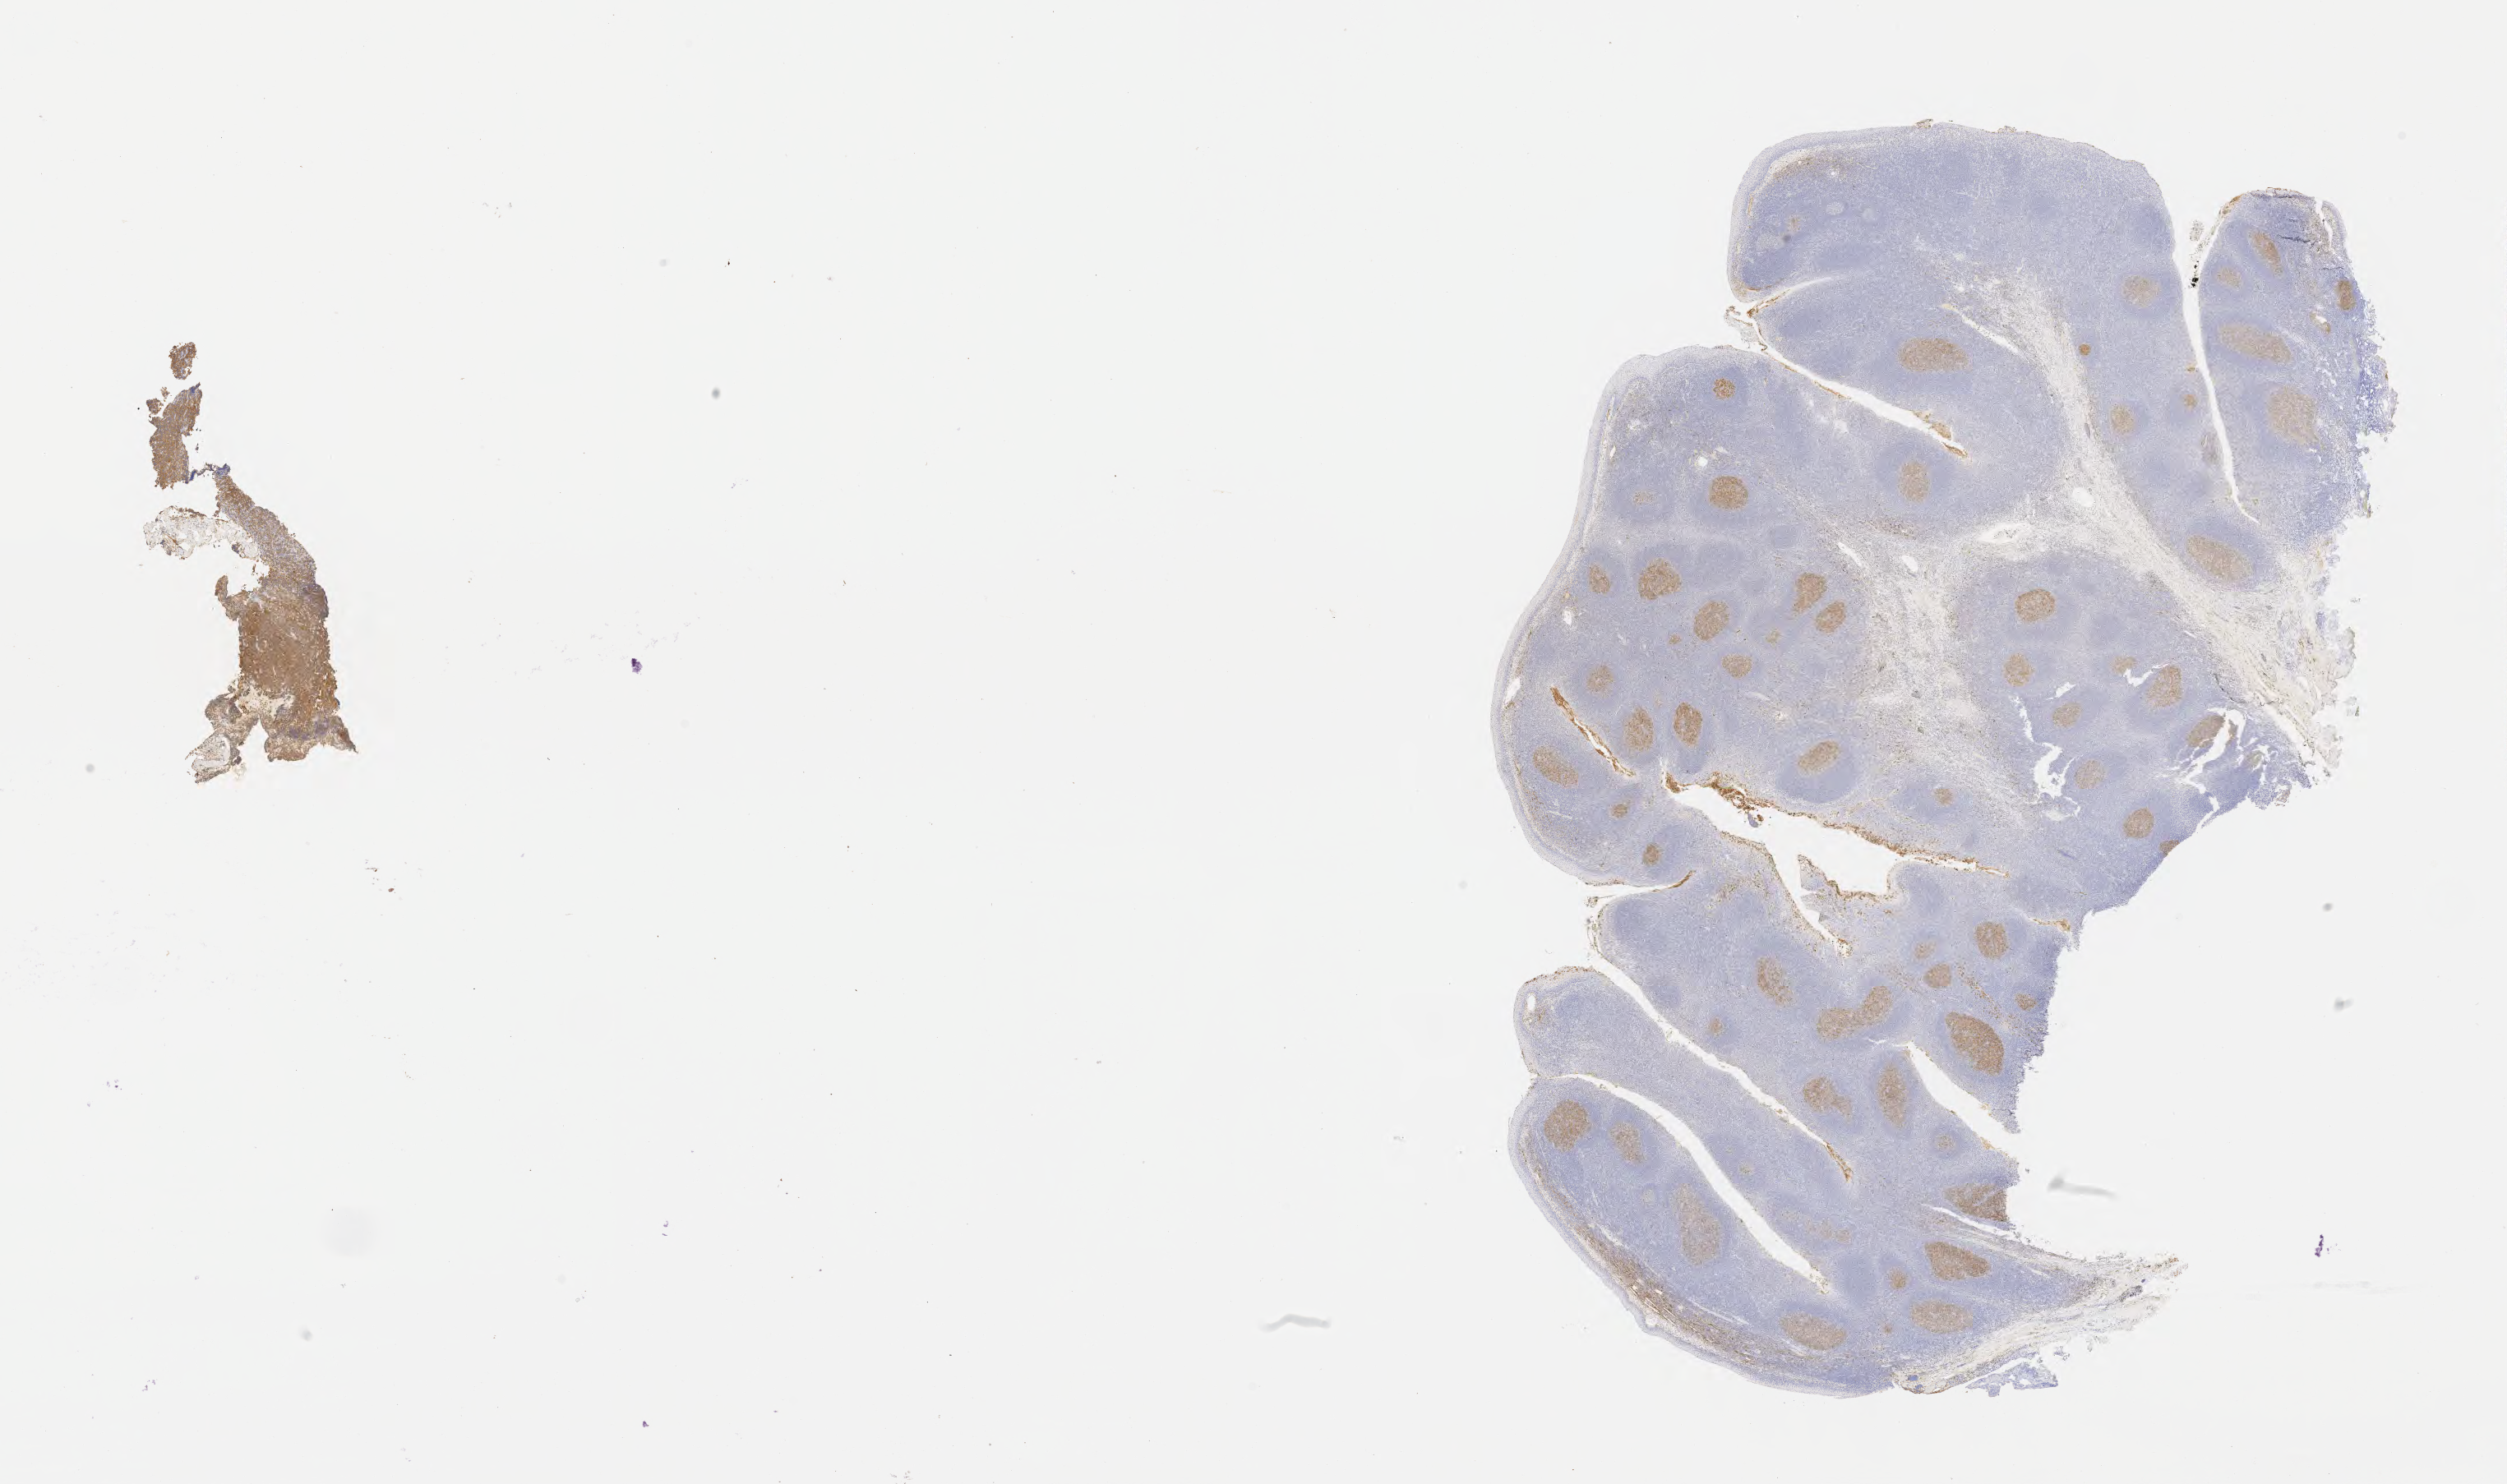
IHC for CD10, whole-slide image, shown as a low-resolution overview of the whole scanned area (about 24.6 x 14.6 mm); specimen: tumor tissue. Patient: female, 27 years old.
Diagnosis: Diffuse large B-cell lymphoma, NOS.